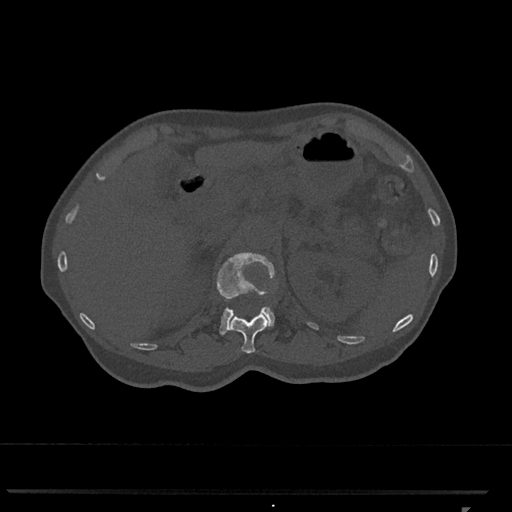
CT including the spine, one axial slice; slice 434 of 793 in the series (ordered by position); reconstruction kernel Br40s/3; bone window (W 1800 / L 400 HU); 512 × 512 image matrix, field of view 380 × 380 mm. Patient: female, 62 years. Case-level facts recorded for this patient, not image findings: primary cancer: renal.
Outlined on this slice (semi-automatically segmented with operator editing):
- L1 vertebra: bounding box (x1, y1, x2, y2) in pixels: (217, 252, 275, 335)
- T12 vertebra: (229, 313, 268, 354)